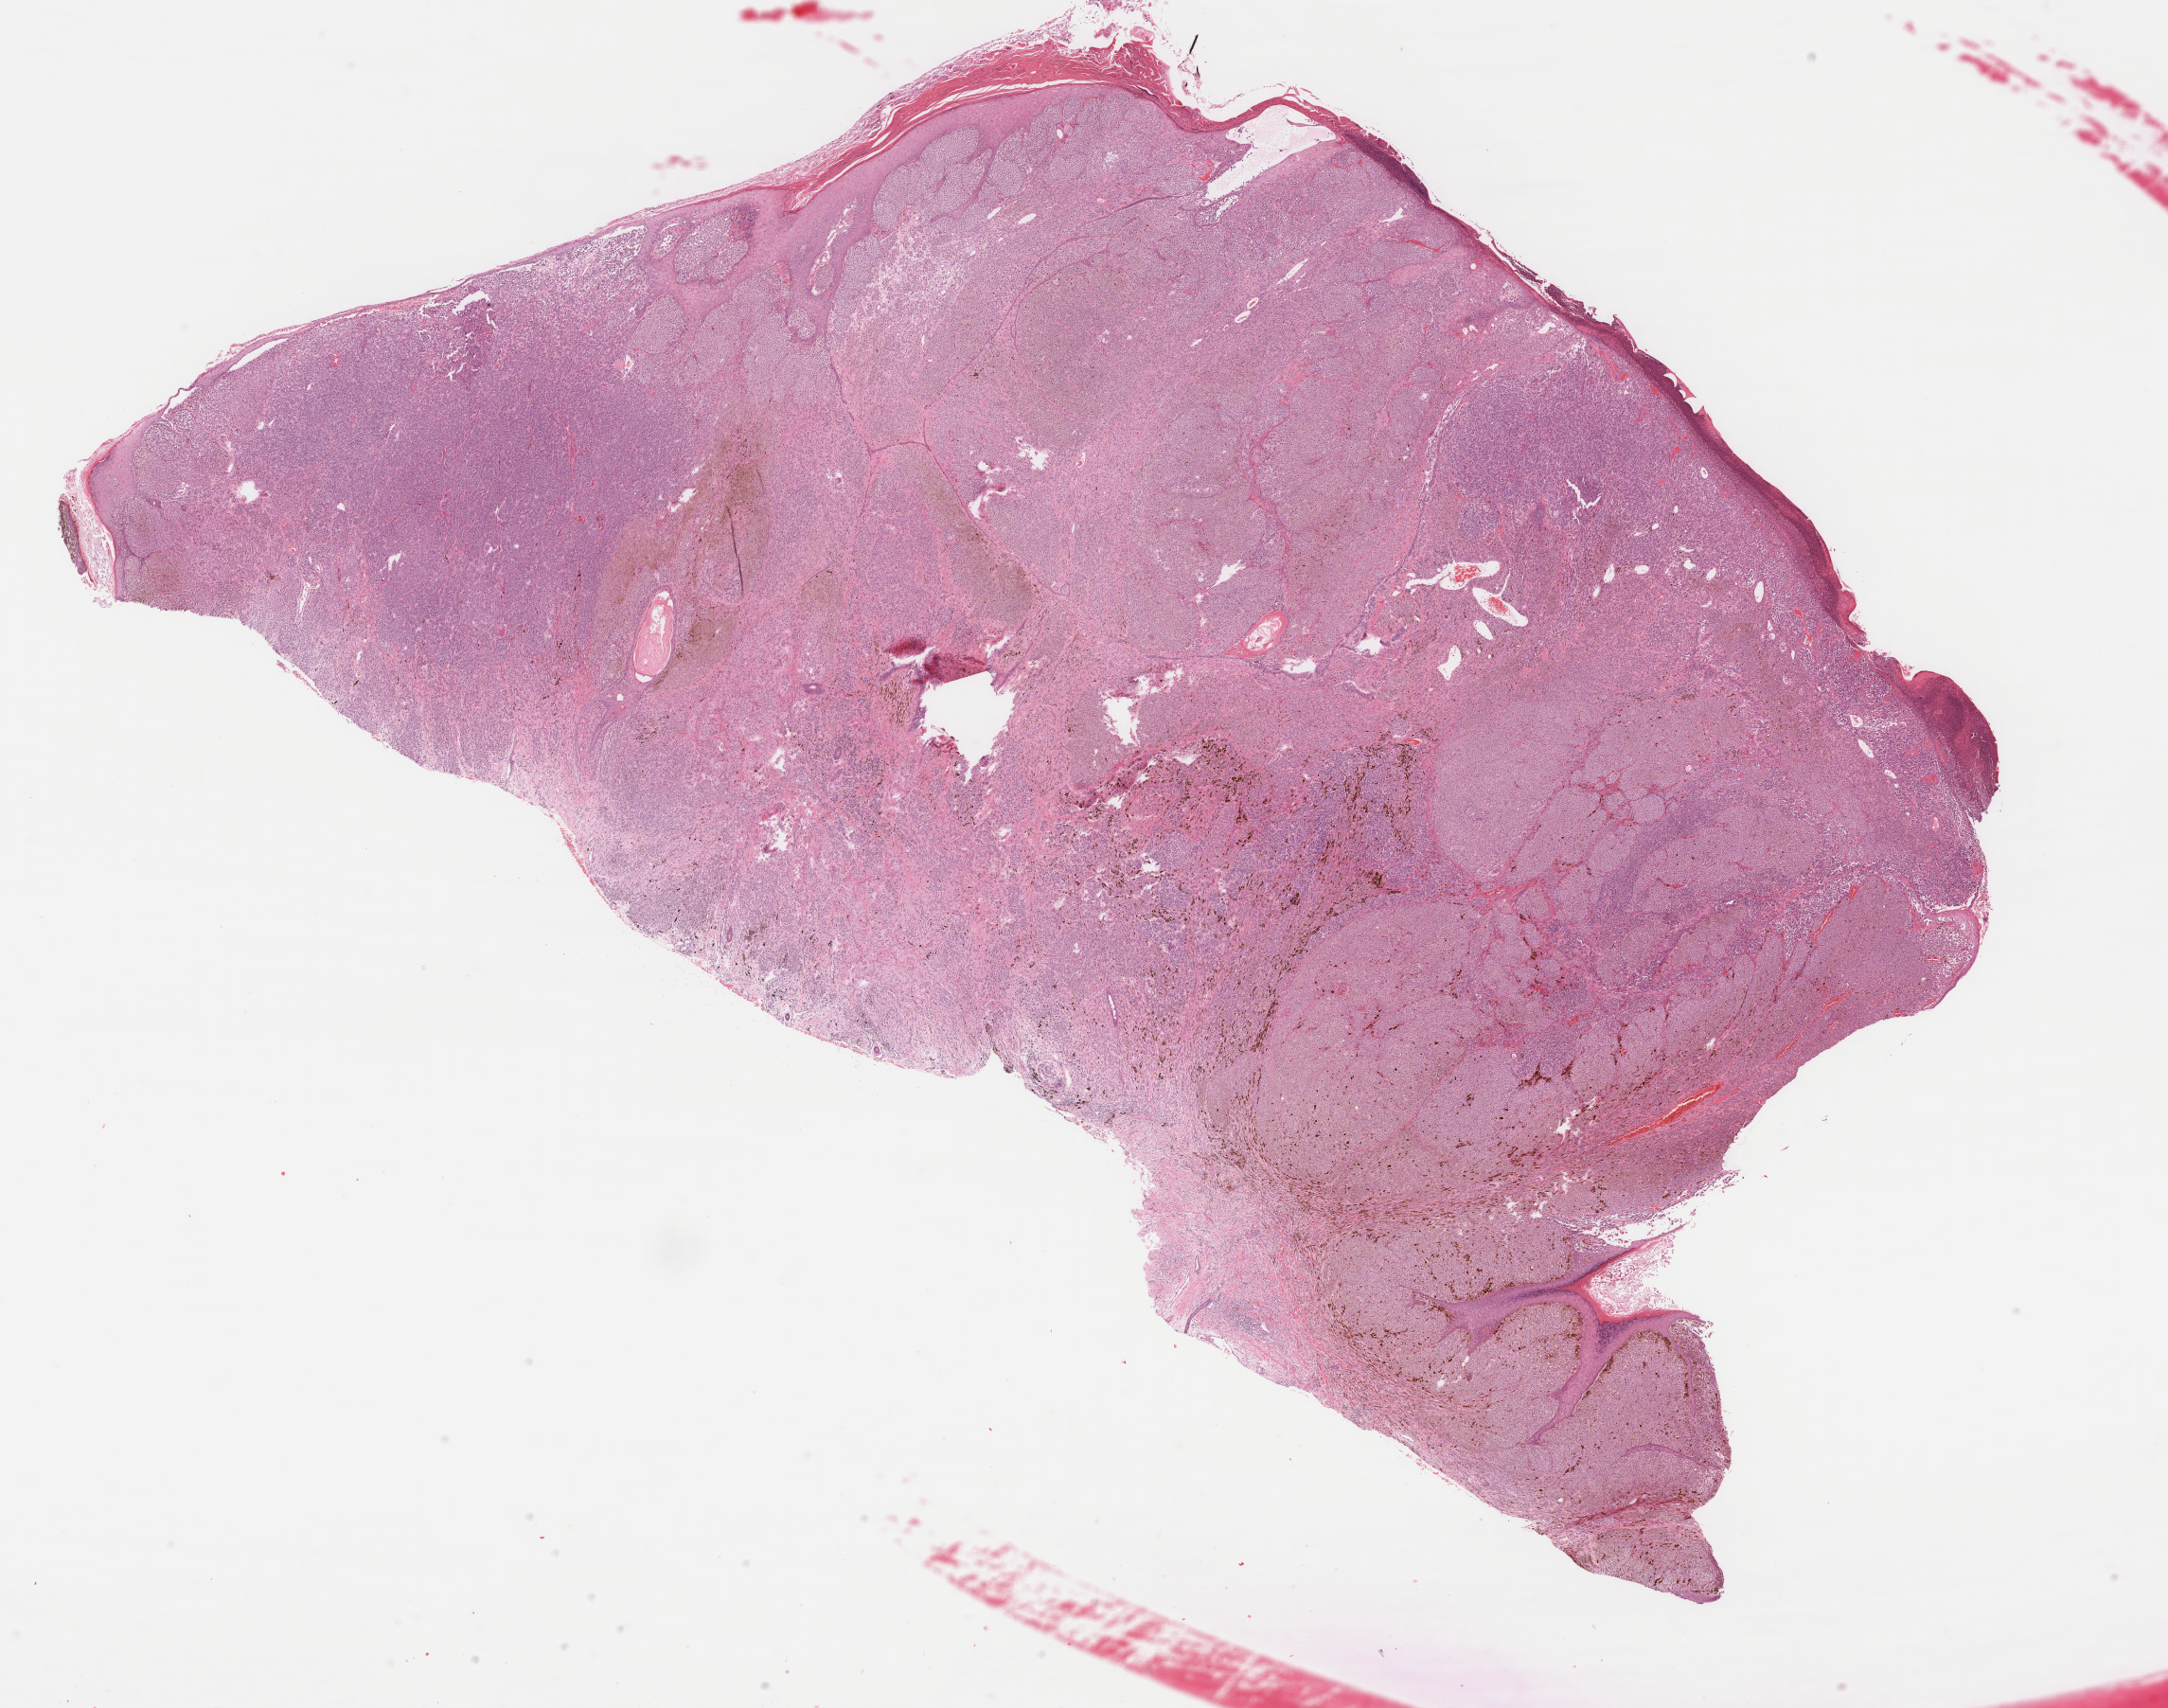
Whole-slide histology image, H&E, low-resolution overview of the scanned area, about 18.2 x 14.3 mm (slide scanned at 40x); formalin-fixed paraffin-embedded (FFPE) diagnostic section; primary tumour sample from the skin. Patient: male, age at initial diagnosis 37 years.
• TNM: T4b N0 M0
• histologic diagnosis: Nodular melanoma
• AJCC pathologic stage: IIC (7th edition)